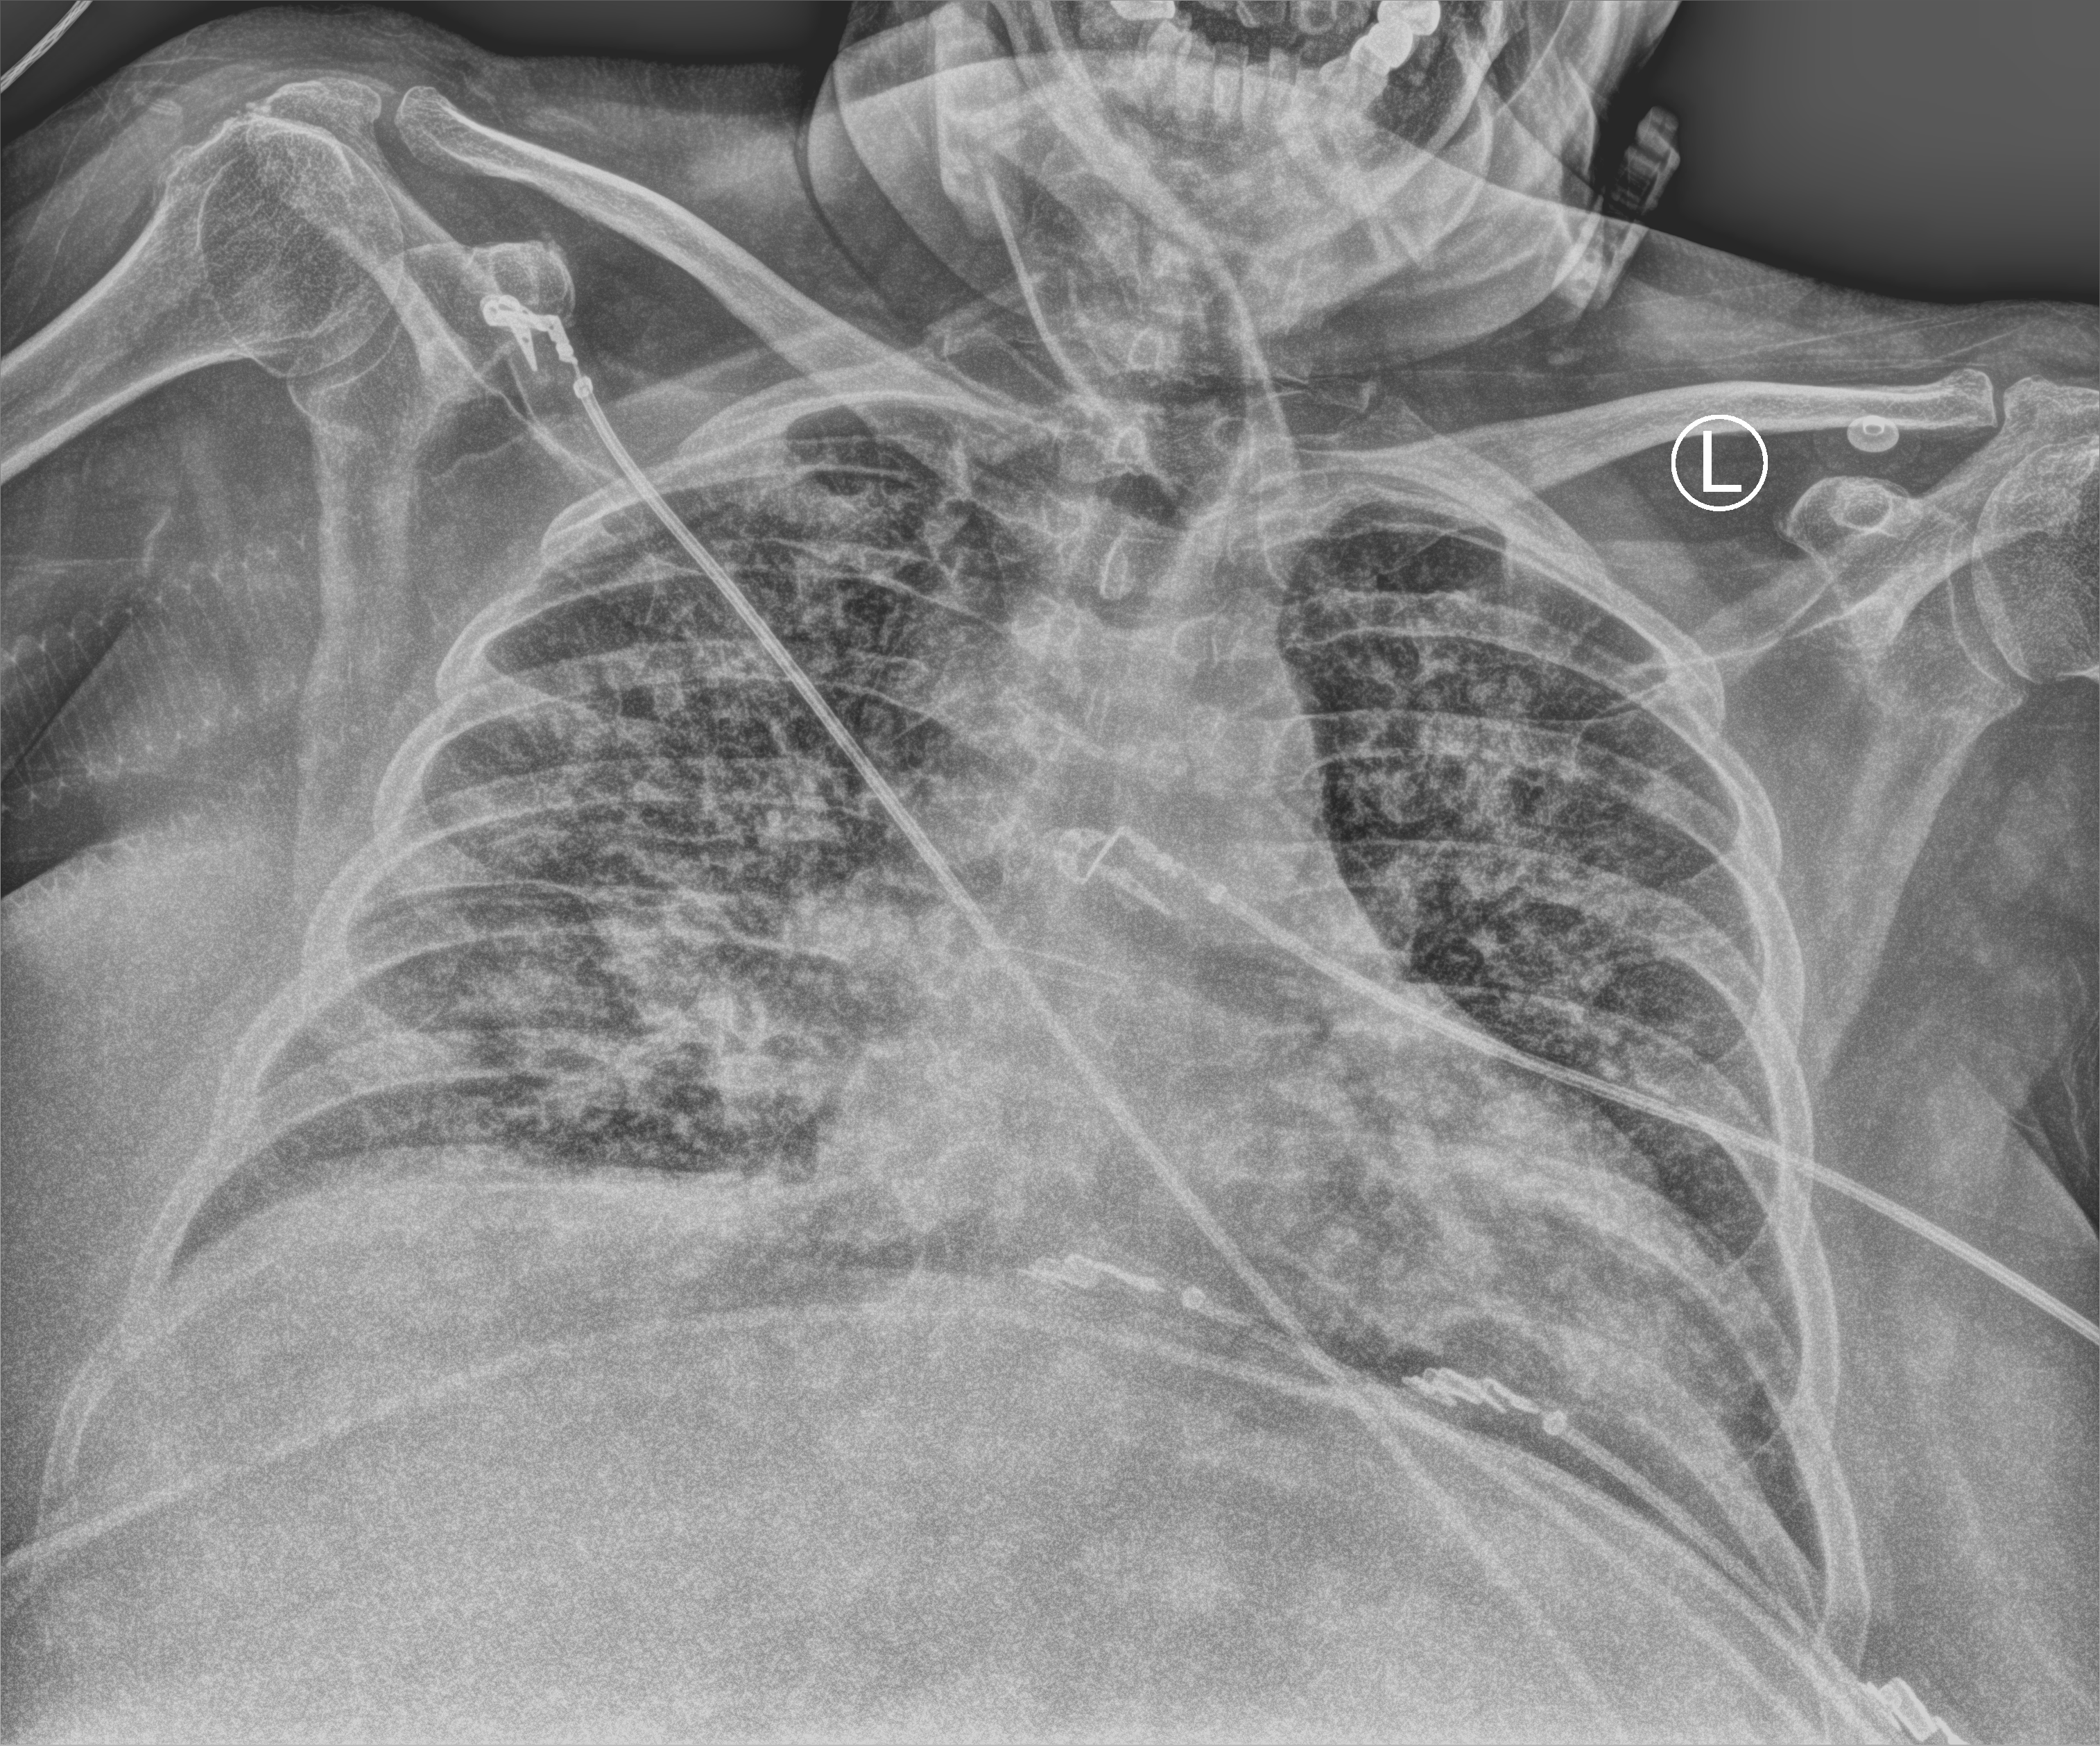
Portable chest radiograph, anteroposterior (AP) projection. Patient hospitalised with COVID-19; female, aged 60–74 years.
From the hospital-stay record, not from the radiograph (when in the stay this image was taken is not recorded): admitted to intensive care during this hospital stay: yes; length of hospital stay: 18 days.